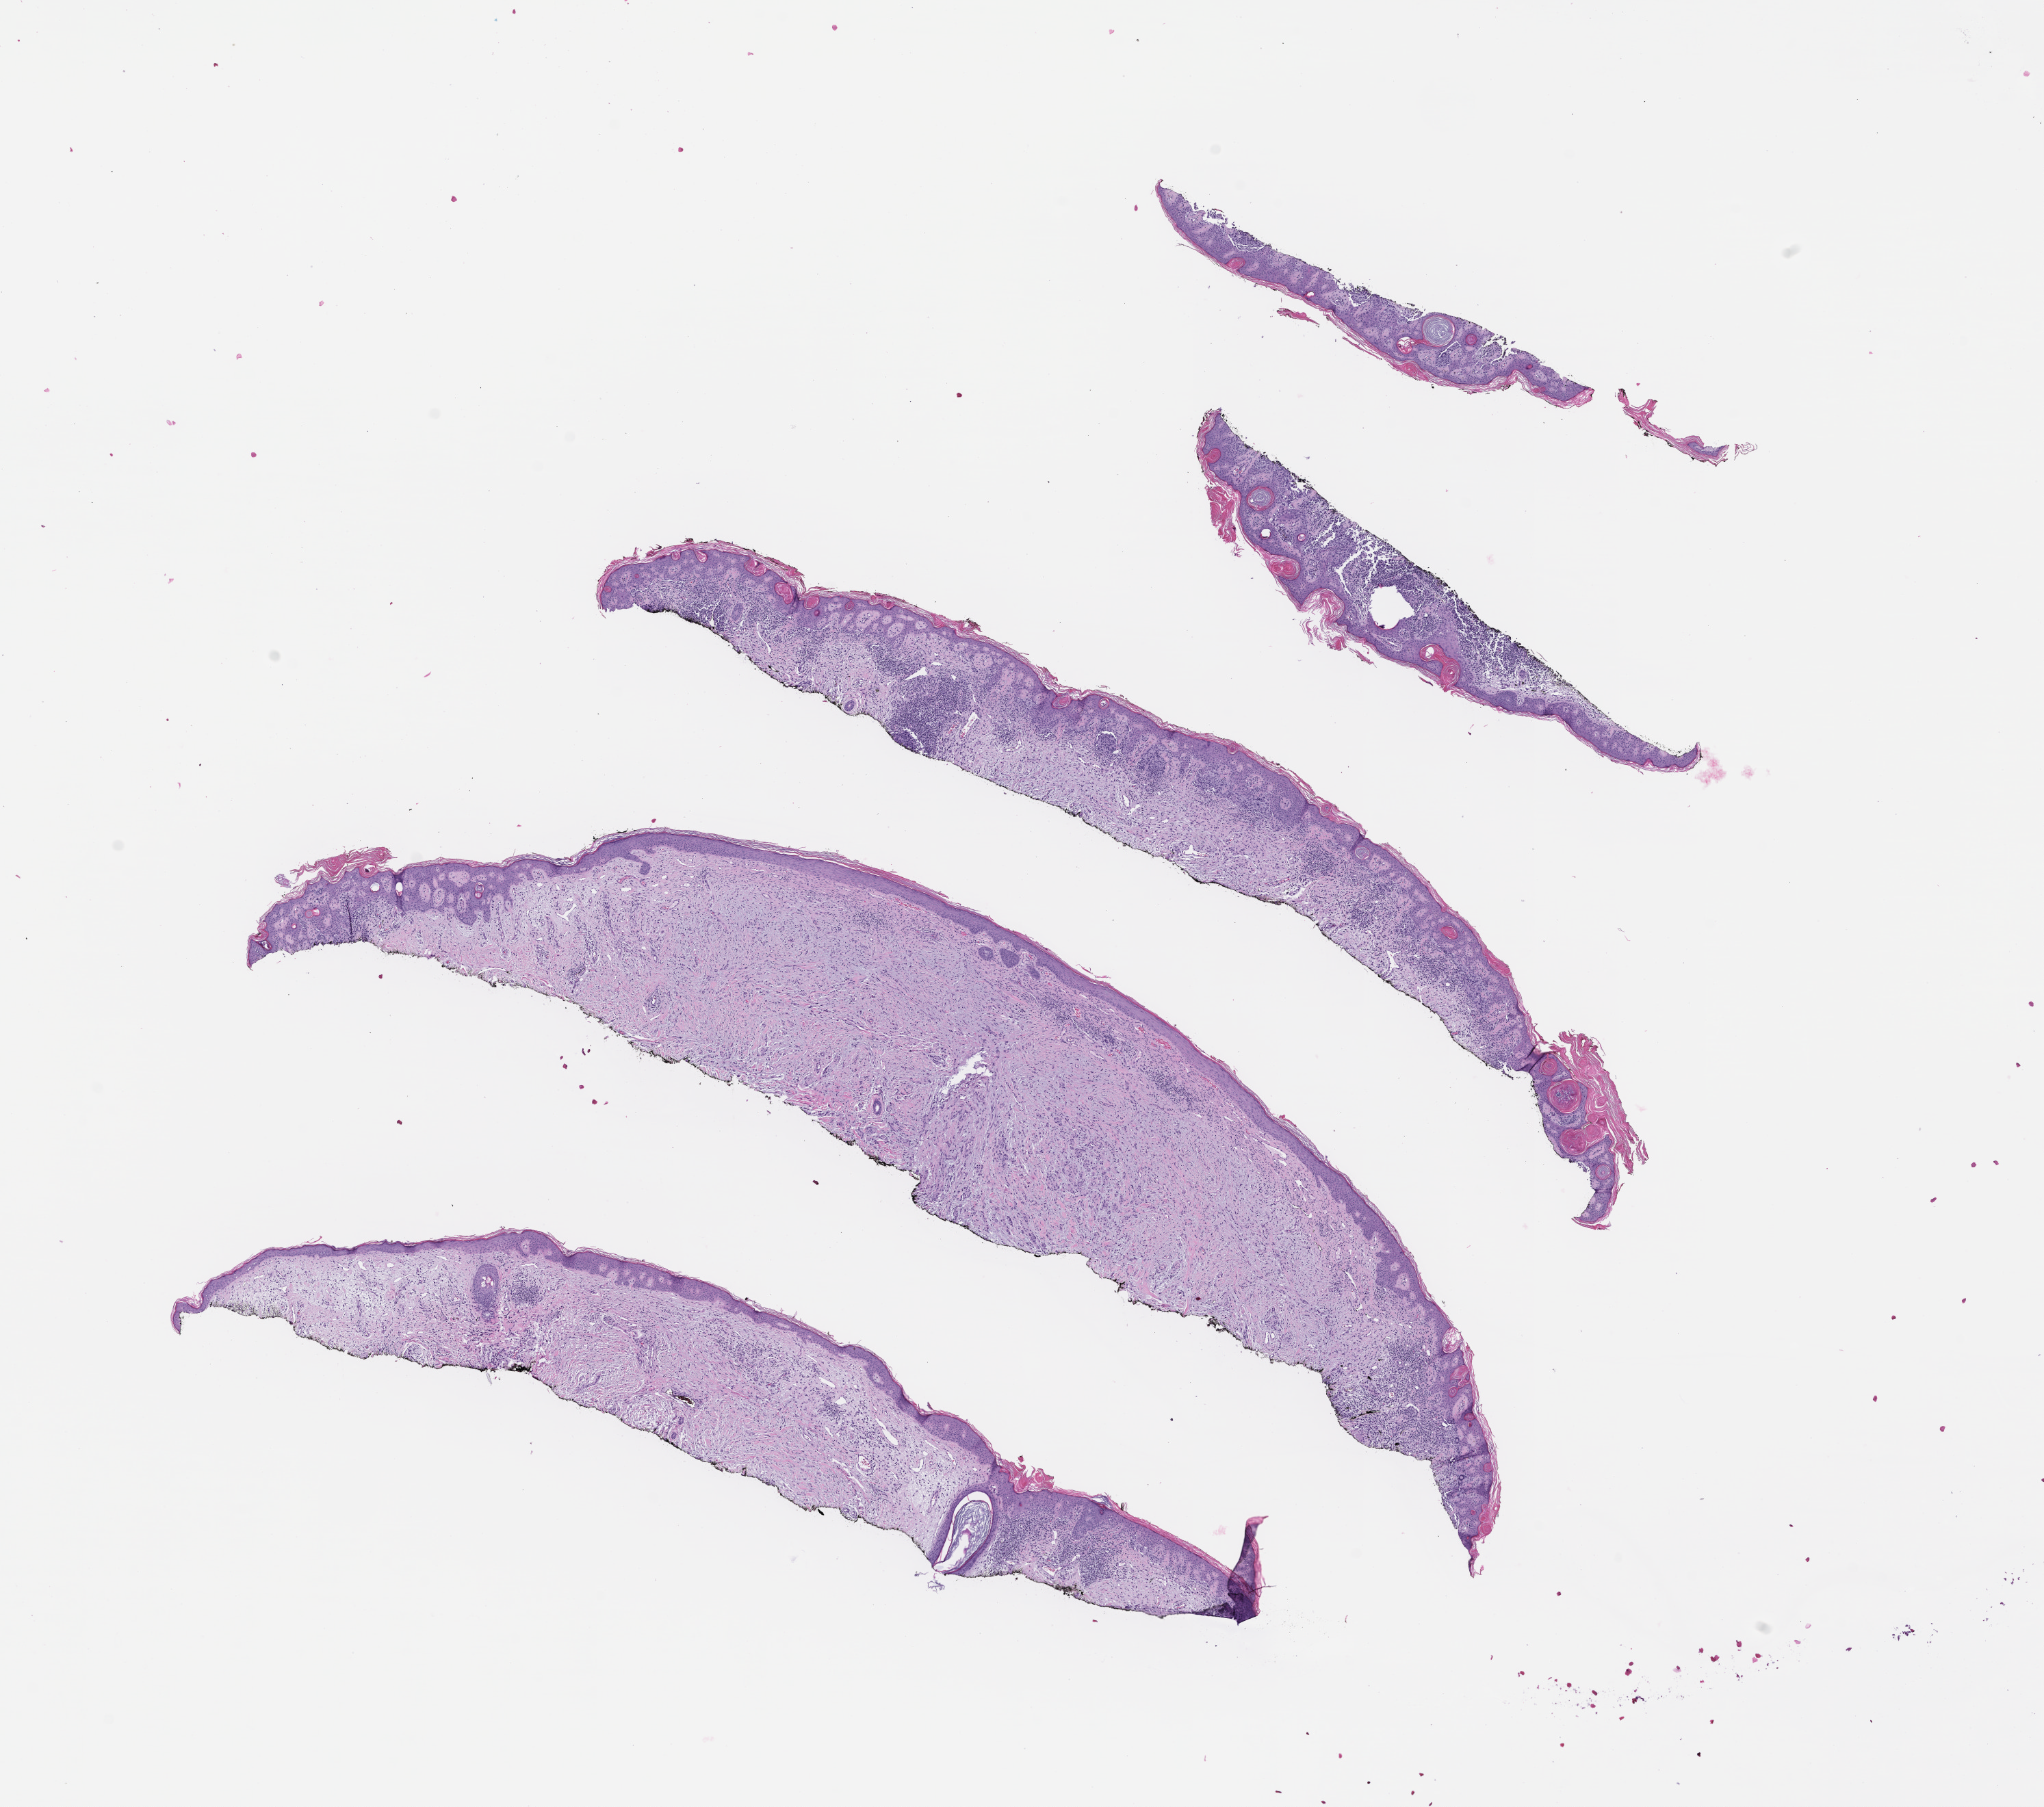
Digitized haematoxylin and eosin-stained section, a low-resolution overview of the entire scanned area, about 12.1 x 10.7 mm; formalin-fixed paraffin-embedded section; tissue site: skin. Patient: female.
This section: primary tumor. Diagnosis: Melanoma.